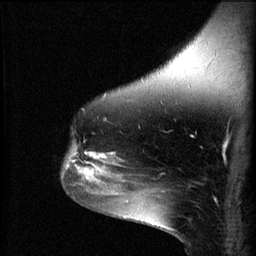
Breast MRI (dynamic contrast-enhanced), one sagittal slice. Position 44 of 60 along the scan axis. 3 images stored at this slice position (order not interpretable as contrast timing). 1.5 T. TE 4.2 ms, TR 8.2 ms. 2 mm slice thickness. 256 × 256 image matrix, field of view 180 × 180 mm. Female patient, age 49 years.
Annotated regions visible in this slice (semi-automatic segmentation, software-assisted and operator-edited):
- analysis volume of interest (the breast-tissue region the enhancement analysis was run in; not a lesion): bounding box (x1, y1, x2, y2) in pixels: (61, 144, 109, 187)
- tumour enhancement mask (voxels above the 70 % enhancement threshold inside the analysis volume of interest): (66, 146, 109, 185)